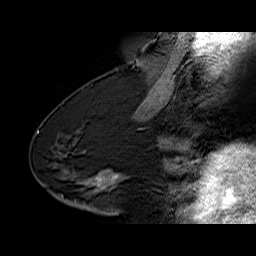
Breast MRI (dynamic contrast-enhanced), one sagittal slice; position 33 of 60 along the scan axis; dynamic contrast-enhanced series, time point 2 of 6 at this slice position (early post-contrast); 1.5 T; TE 6.4 ms, TR 32.9 ms; 4 mm slice thickness; 256 × 256 image matrix, field of view 200 × 200 mm. Female patient. Case-level facts recorded for this patient, not image findings: setting: breast cancer imaged before/during neoadjuvant chemotherapy; receptor status: HR-positive, HER2-negative.
Structures marked on this image (semi-automatic segmentation, software-assisted and operator-edited):
- analysis volume of interest (the breast-tissue region the enhancement analysis was run in; not a lesion): box from (x=68, y=160) to (x=128, y=203) px
- tumour enhancement mask (voxels above the 100 % enhancement threshold inside the analysis volume of interest): (x=92, y=170)–(x=121, y=191)